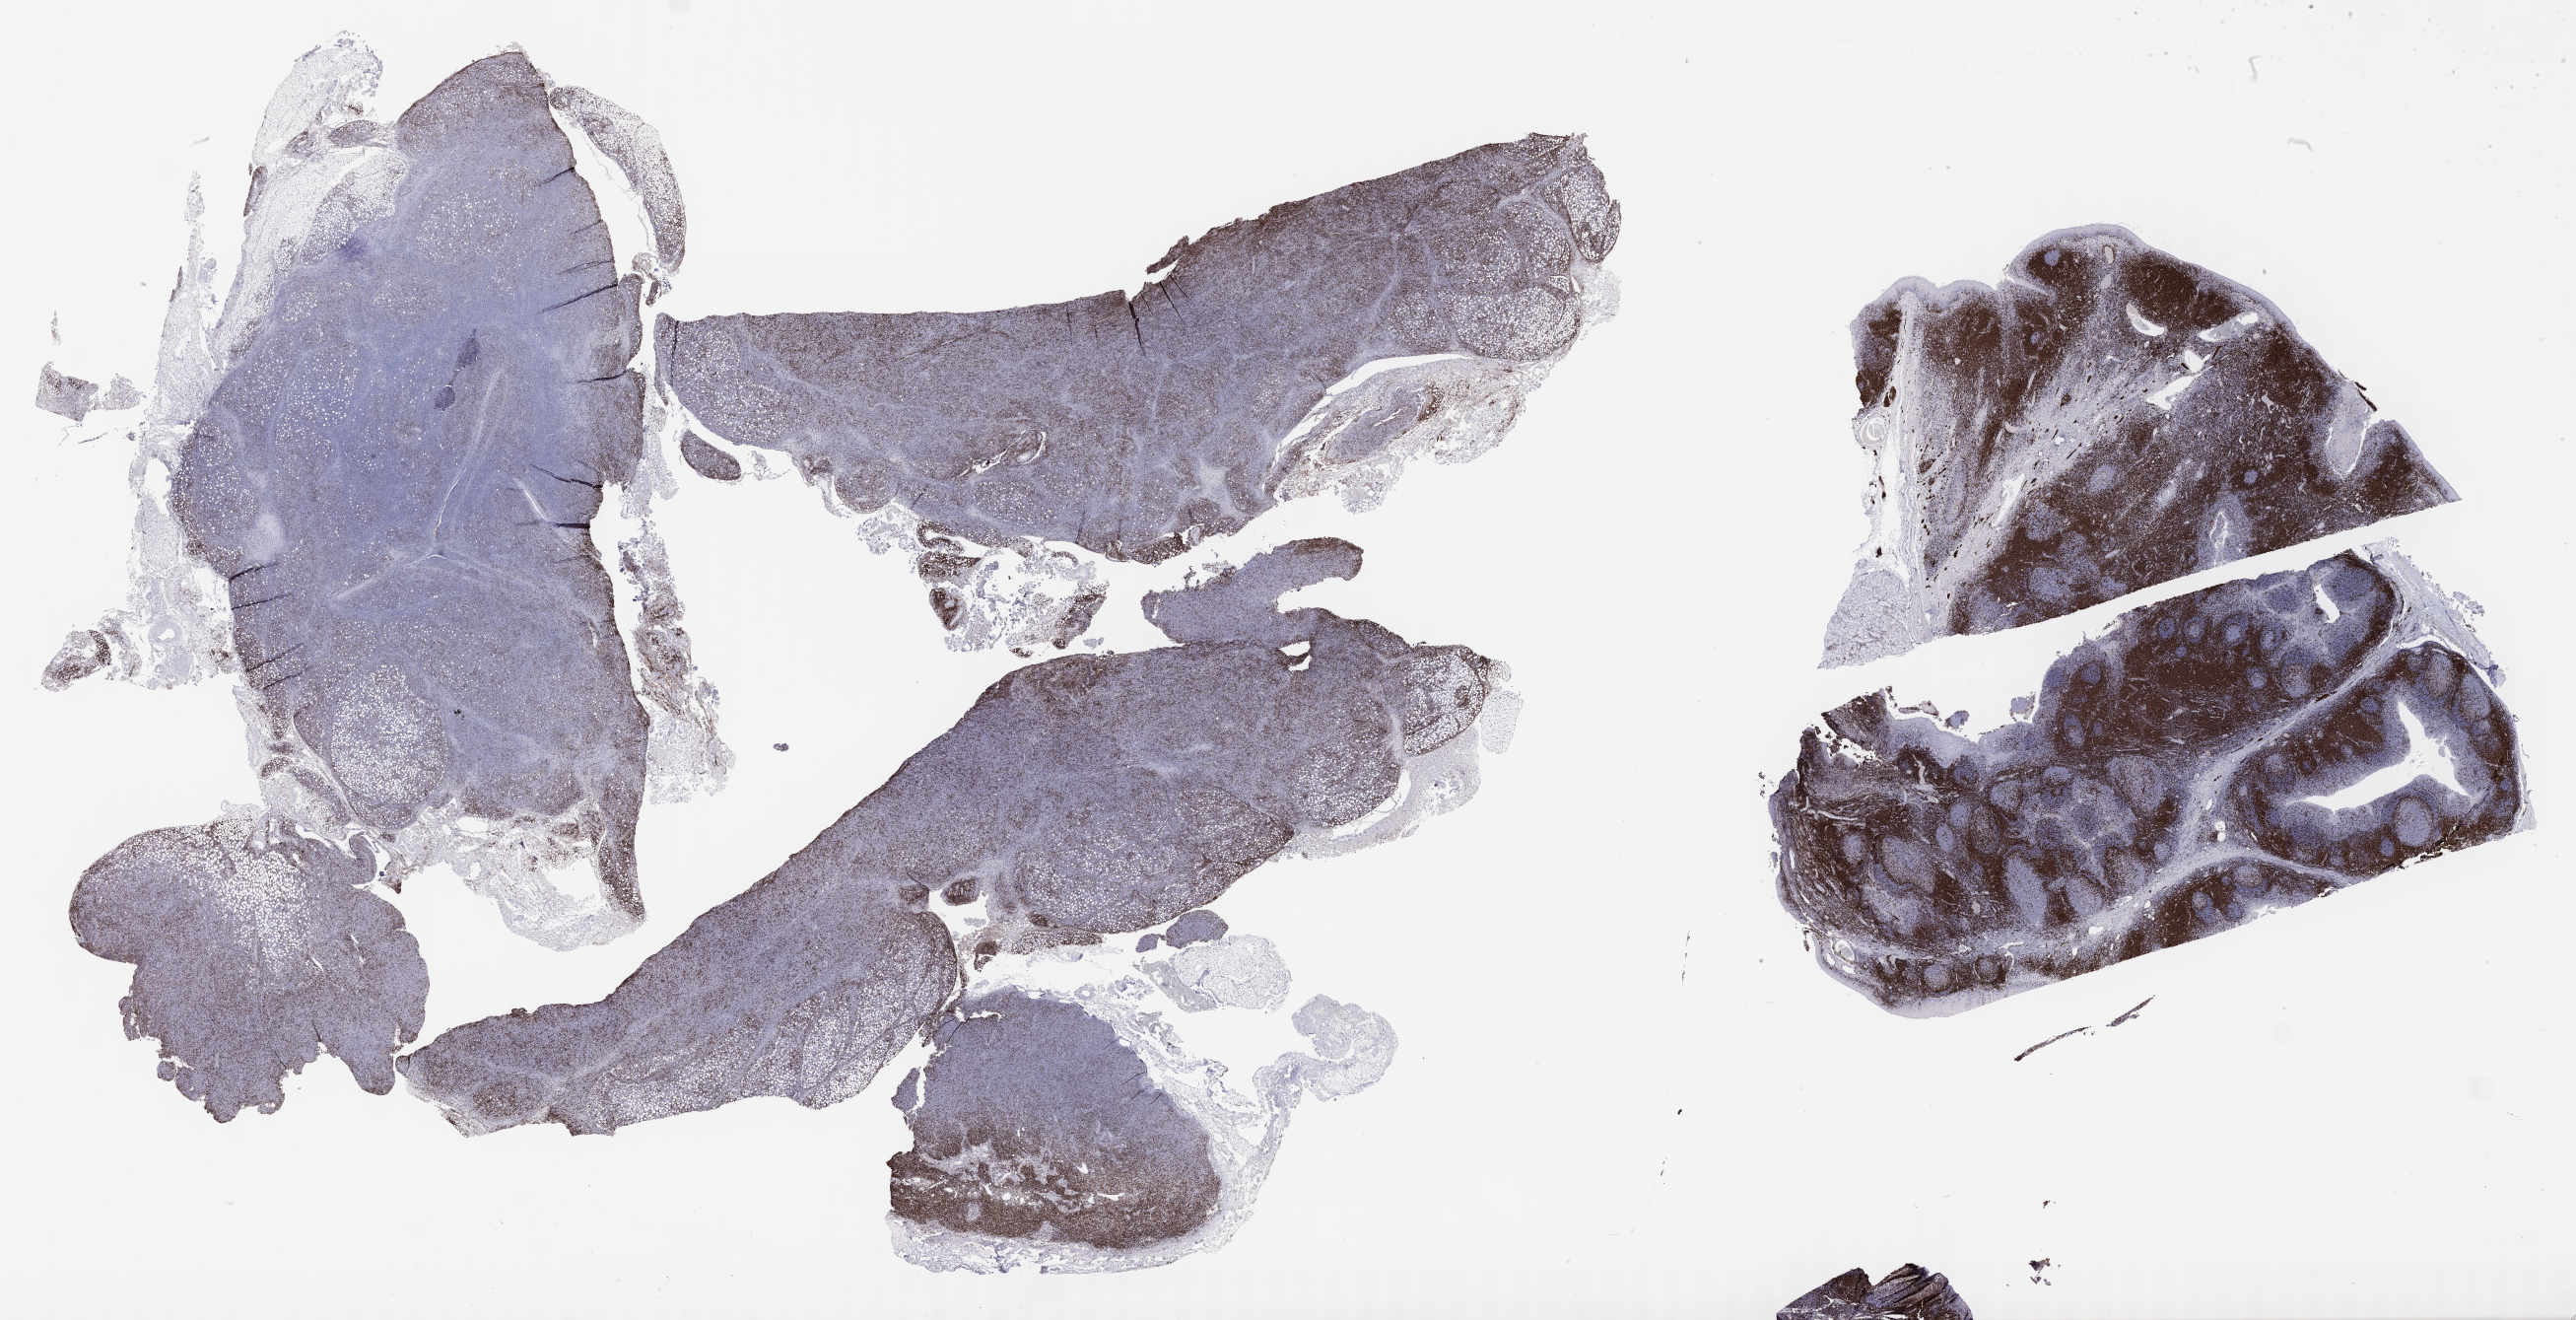
IHC for CD3, whole-slide image, shown as a low-resolution overview of the whole scanned area (about 42.3 x 21.7 mm); specimen: tumor tissue; anatomic site: lymph node. Patient male; age 68 years.
Histologic diagnosis: Diffuse large B-cell lymphoma, NOS.